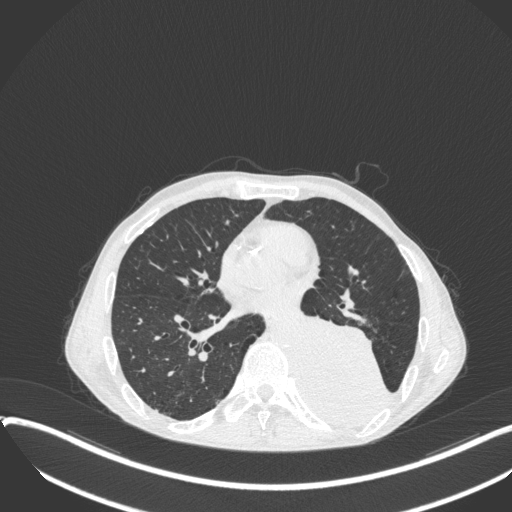
Chest CT, one axial slice. Reconstruction kernel B31f. Lung window (W 1500 / L -600 HU). 1 mm slice thickness. 512 × 512 image matrix, field of view 400 × 400 mm. Patient: male, 57 years. Case-level facts recorded for this patient, not image findings: clinical TNM (as recorded): T4 N0 M0.
Annotated regions visible in this slice (rectangle marked by the reading radiologist):
- lung tumour (recorded histology: squamous cell carcinoma): bounding box [x1, y1, x2, y2] px = [296, 310, 393, 435]